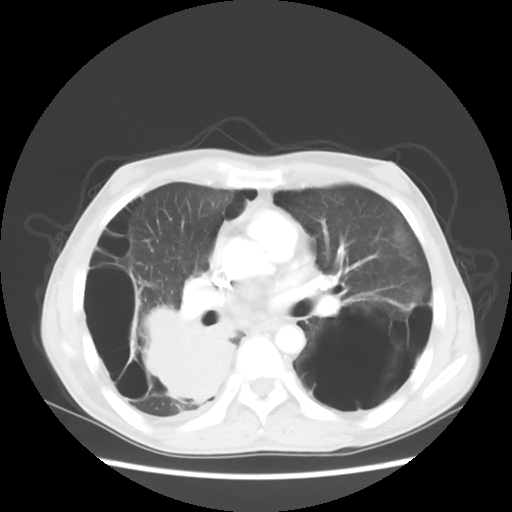
Chest CT, one axial slice; slice 29 of 56 in the series (ordered by position); reconstruction kernel STANDARD; lung window (W 1500 / L -600 HU); 5 mm slice thickness; 512 × 512 image matrix, field of view 351 × 351 mm. Patient: male, 41 years. Case-level facts recorded for this patient, not image findings: clinical TNM (as recorded): T4 N0 M1a; histopathological grade: G3.
Annotated regions visible in this slice (bounding box drawn by a radiologist):
- lung tumour (recorded histology: large cell carcinoma): bounding box <129,295,245,403> (left, top, right, bottom; pixels)